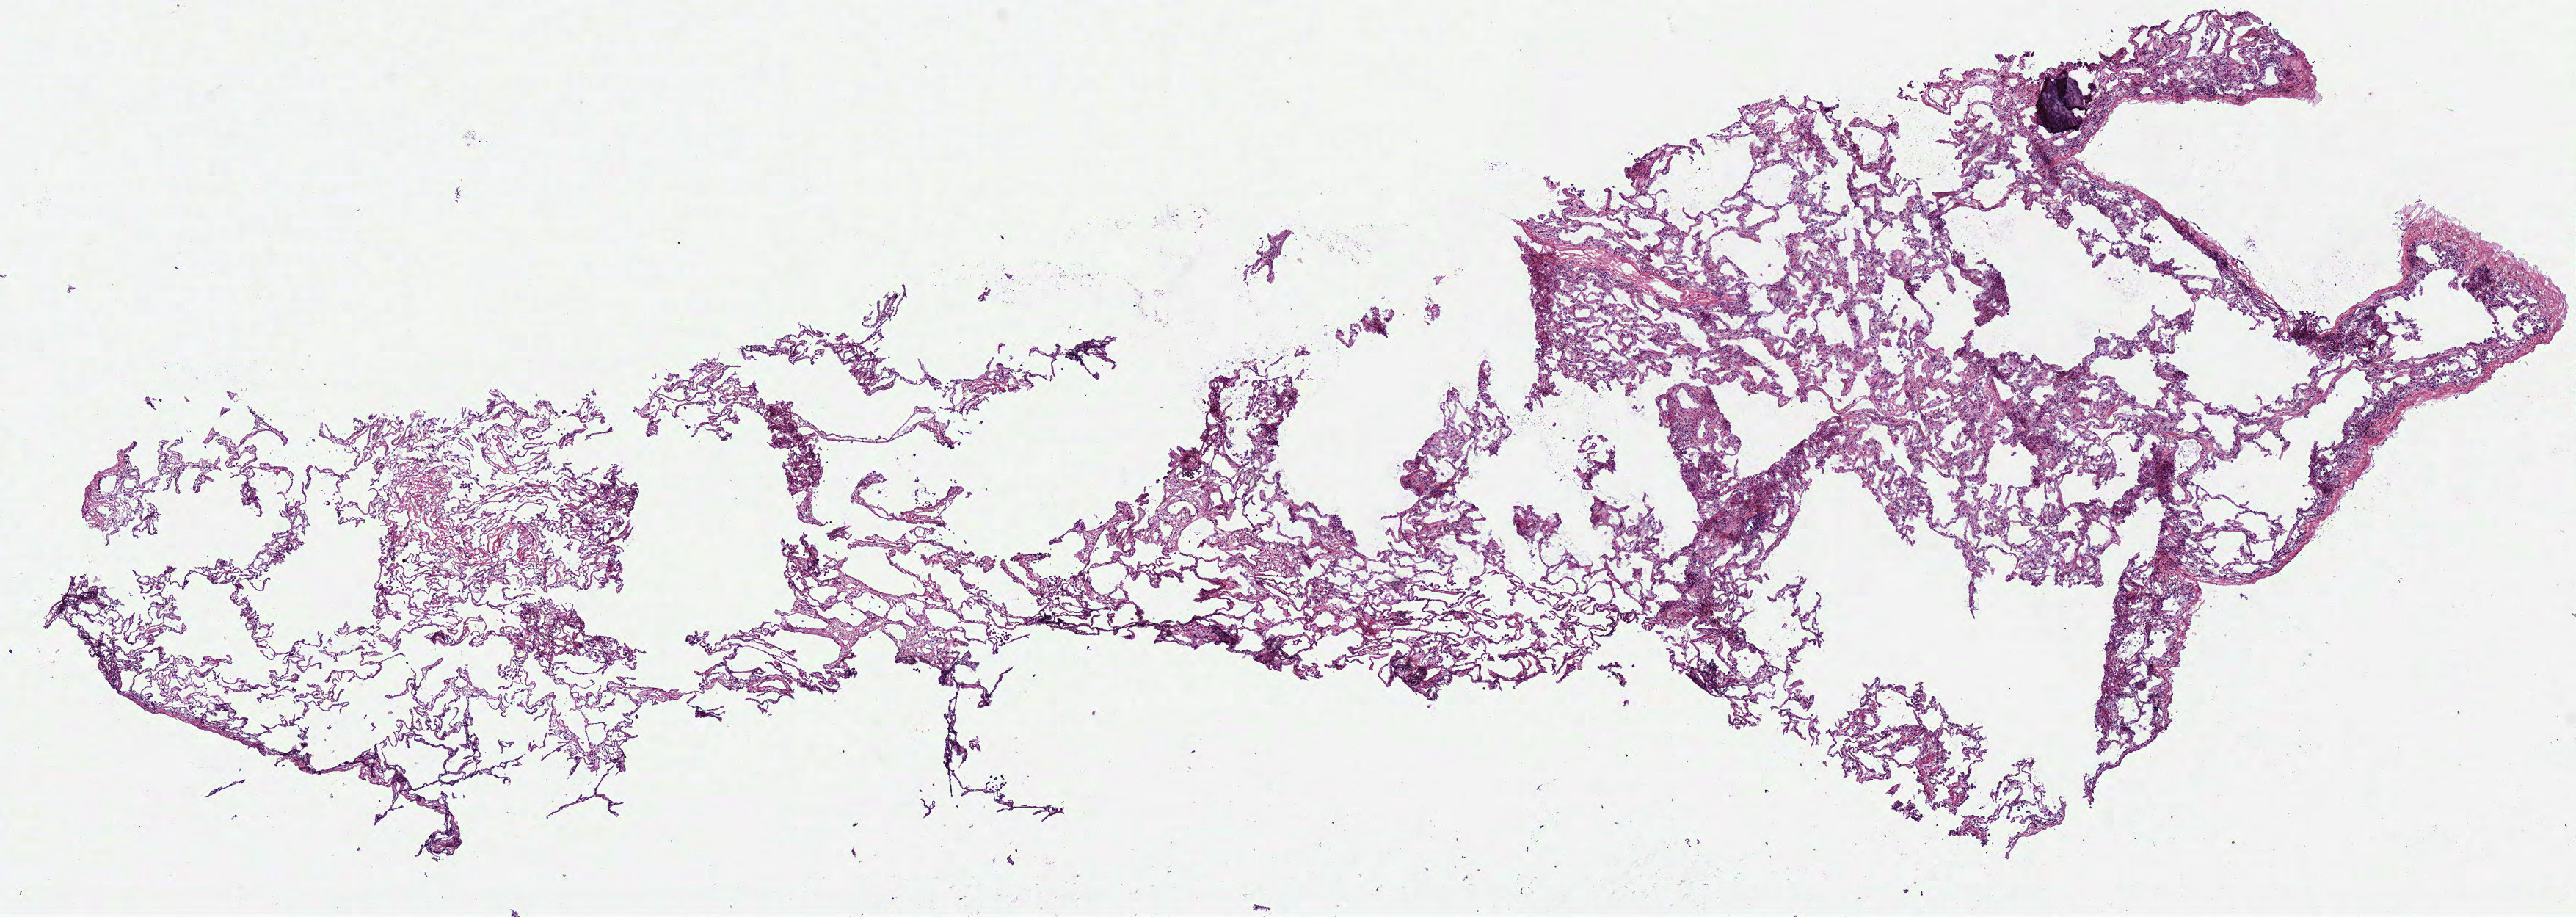
Whole-slide histology image, Hematoxylin and eosin (H&E) stained — low-resolution overview of the scanned area, about 13.8 x 4.9 mm, frozen section from the top of the tissue portion, lung, solid tissue normal (non-tumour tissue) sample. Female, age 81 years at initial diagnosis.
This section: solid tissue normal (non-tumour) sample from the same patient. Patient diagnosis: Clear cell adenocarcinoma, NOS (upper lobe, lung).